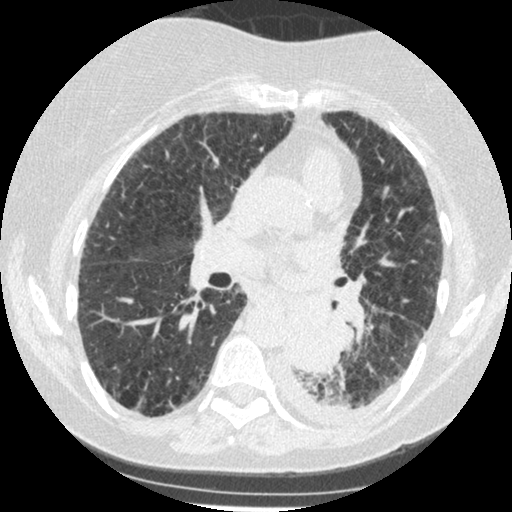
Low-dose screening chest CT, one axial slice; position 133 of 341 along the scan axis; reconstruction kernel STANDARD; 120 kVp; lung window (W 1500 / L -600 HU); 512 × 512 image matrix, field of view 310 × 310 mm.
Structures marked on this image (manually delineated by an expert):
- lesion 1 (tumor, lower lobe of left lung): bounding box <286,308,343,374> (left, top, right, bottom; pixels)